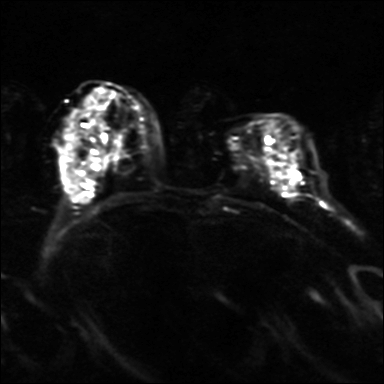
Breast MRI, one axial slice. Slice 12 of 36 in the series (ordered by position). Diffusion-weighted series; image 2 of 4 stored at this slice position (different b-values; order by instance number). 3 T. 4 mm slice thickness. 384 × 384 image matrix, field of view 320 × 320 mm. Female patient.
Structures marked on this image (manually delineated by an expert):
- tumour on diffusion-weighted imaging: bounding box (x1, y1, x2, y2) in pixels: (289, 171, 298, 188)